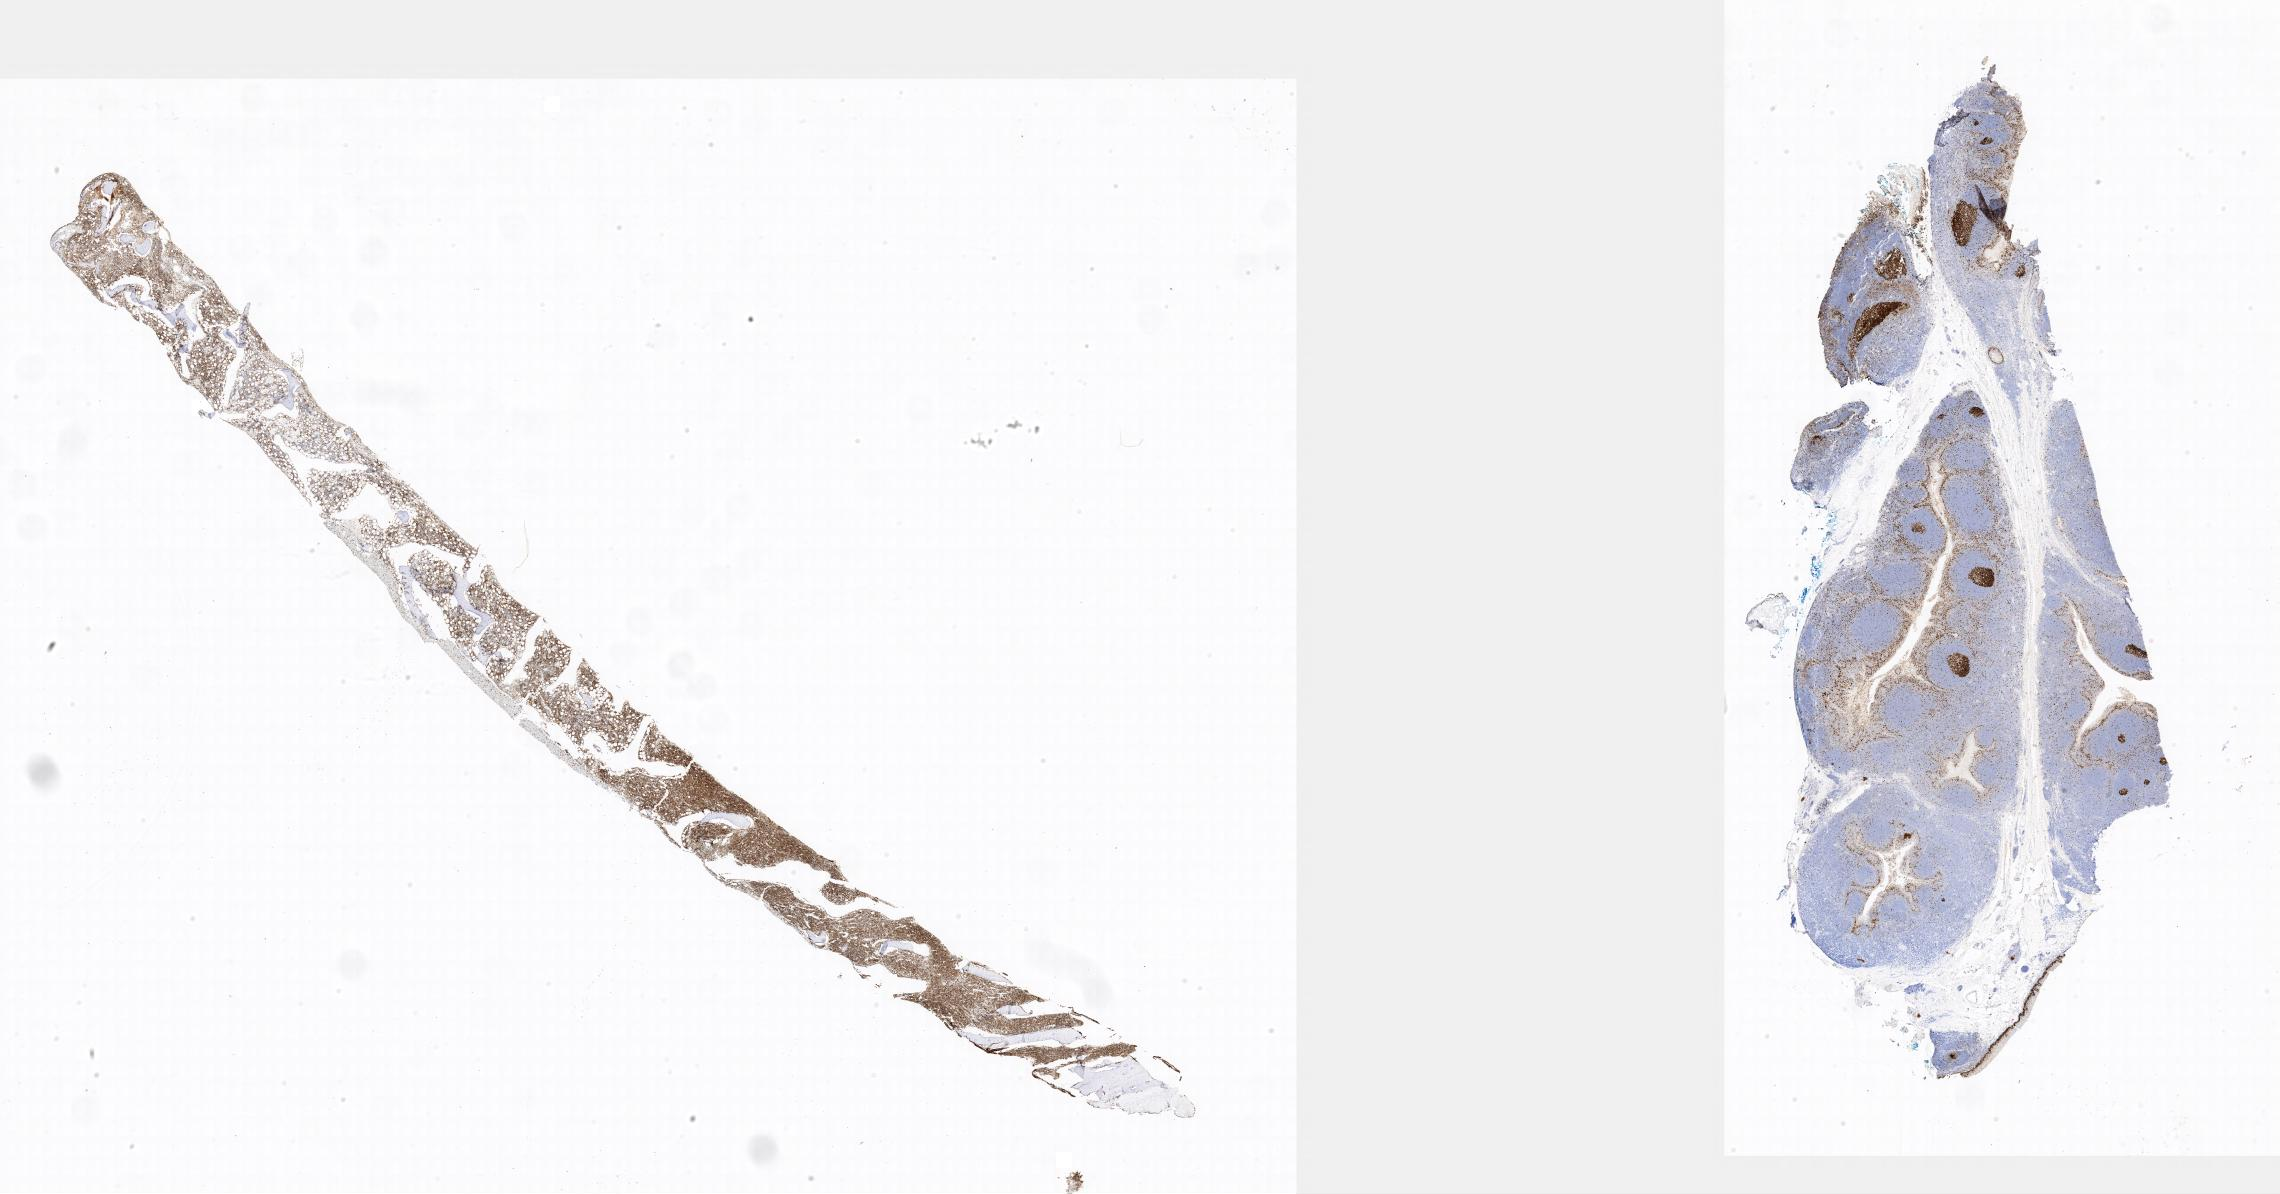
Immunohistochemistry (IHC) whole-slide image stained for Ki-67, a low-resolution overview of the entire scanned area. Specimen: tumor tissue. Male patient, age 12 years.
Histologic diagnosis: Burkitt lymphoma, NOS.